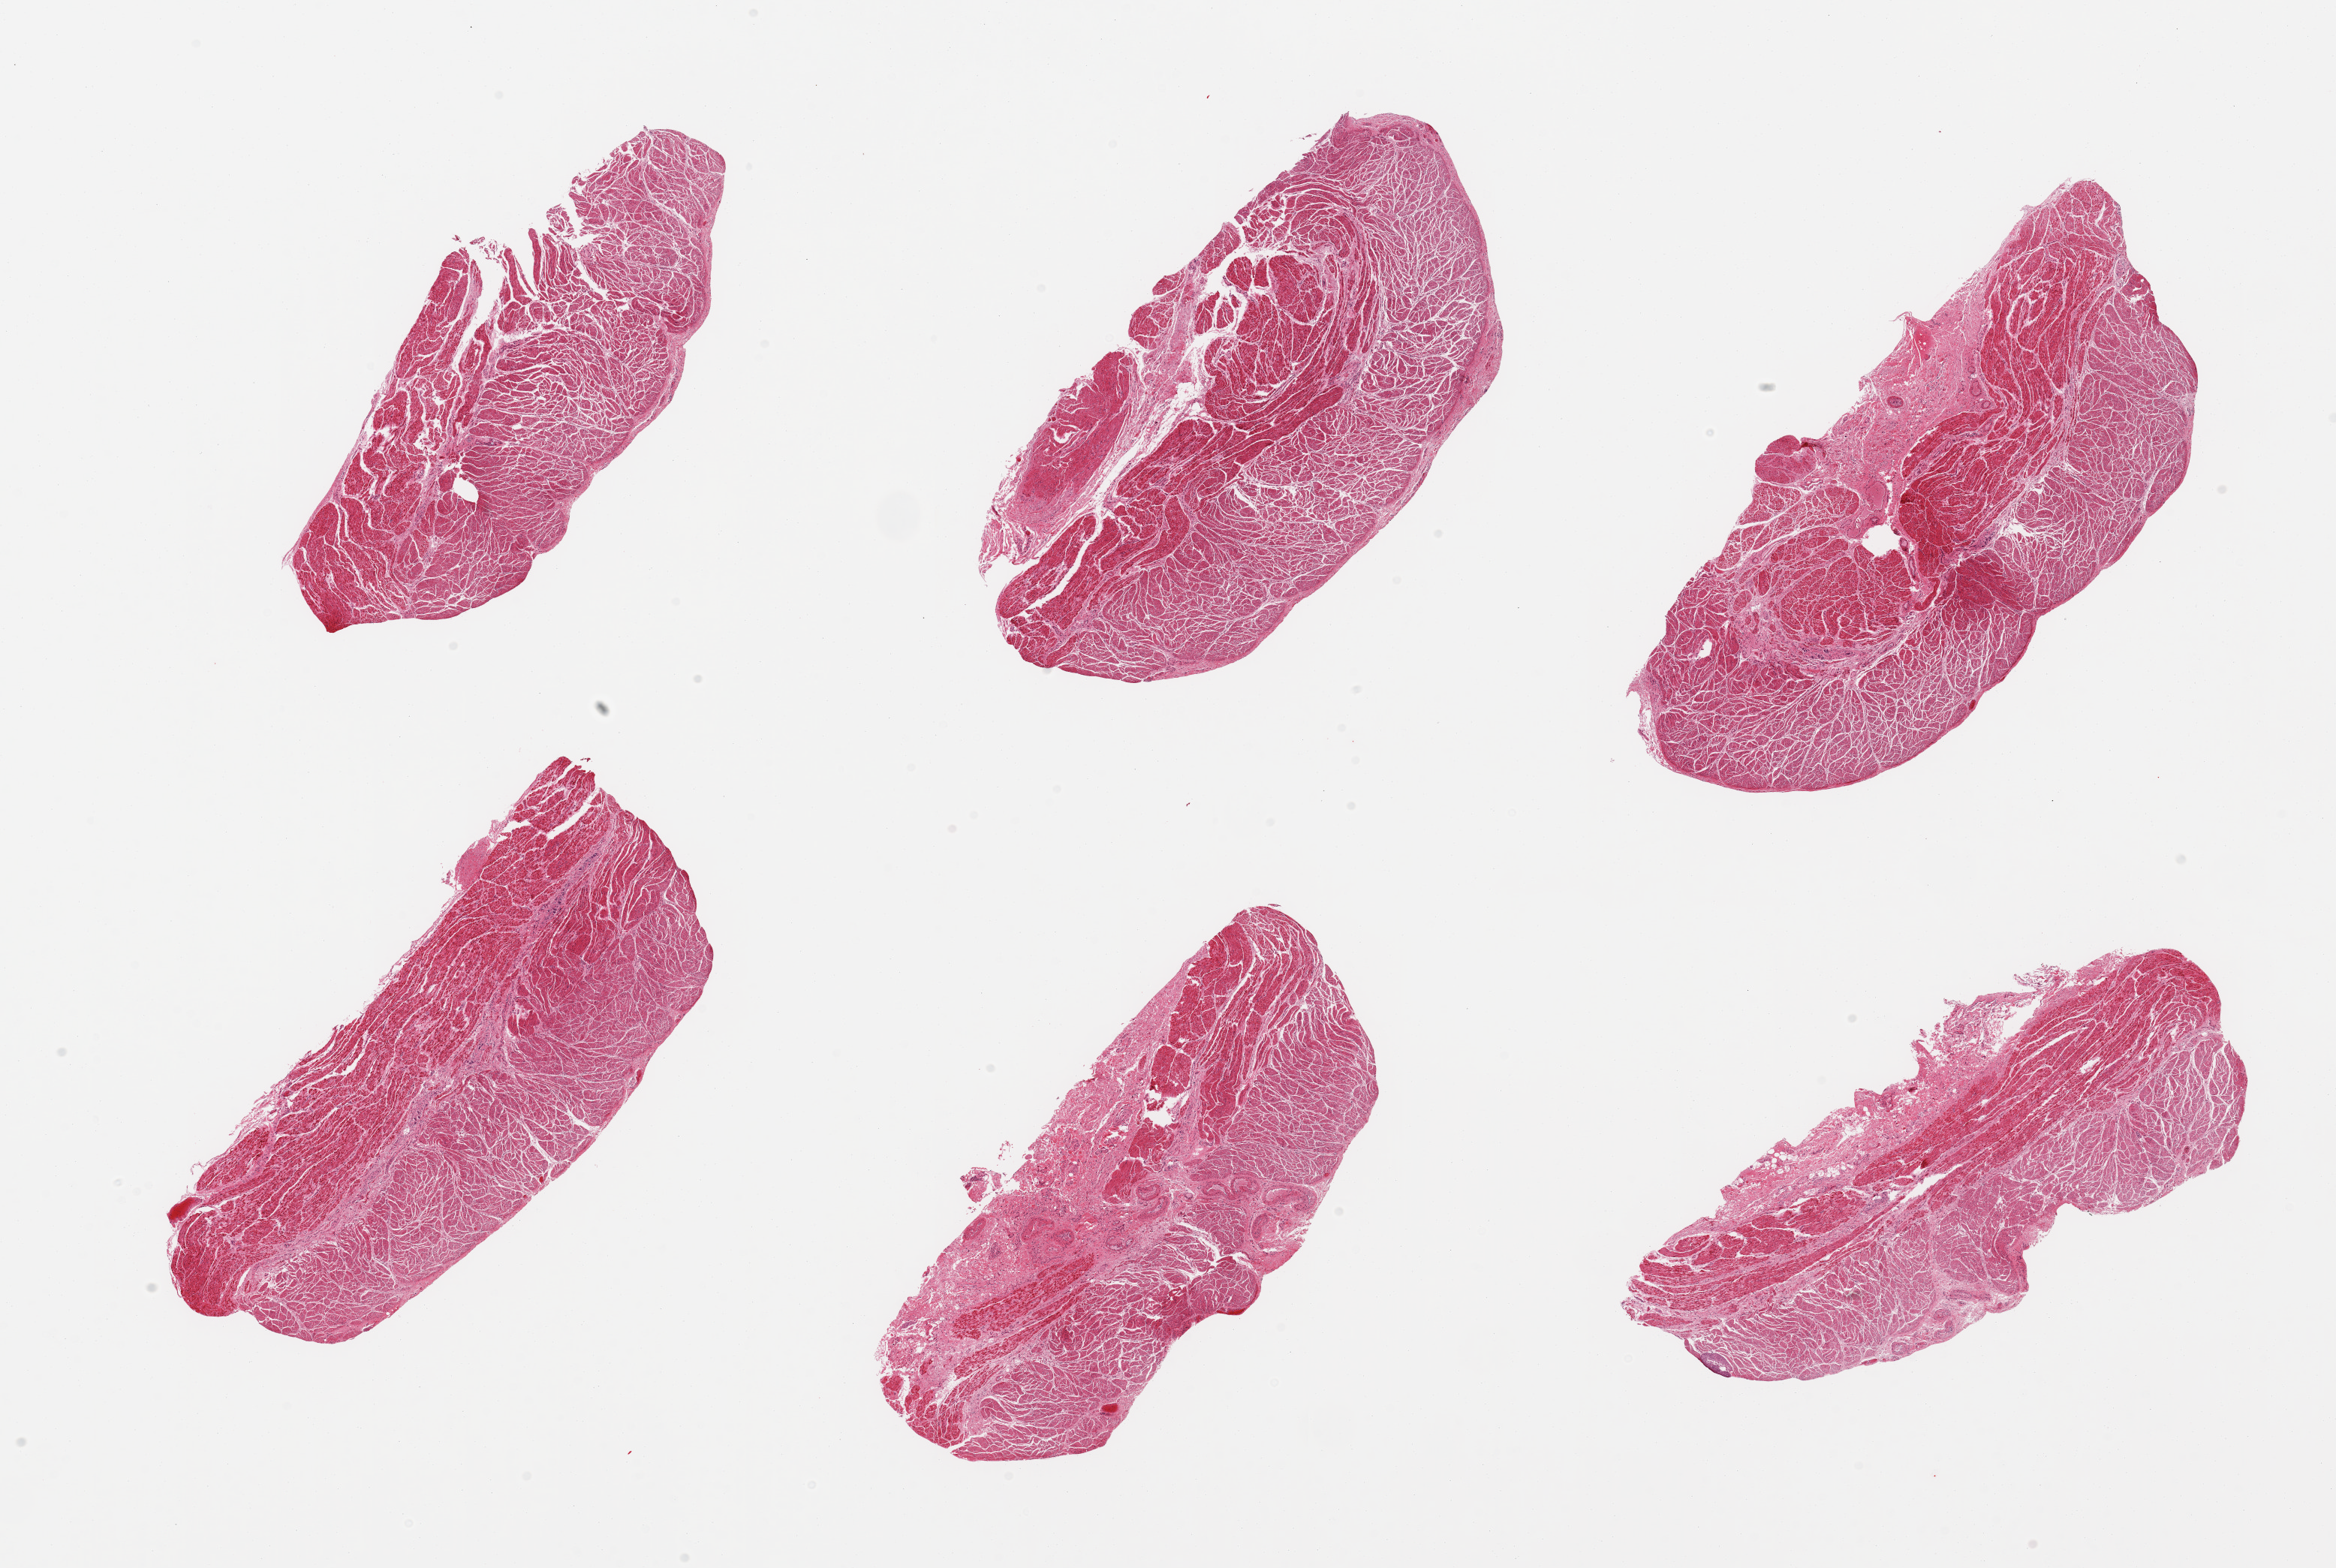
Digitized hematoxylin and eosin (H&E)-stained section, brightfield, a low-resolution overview of the entire scanned area, about 24.6 x 16.5 mm. PAXgene-fixed paraffin-embedded (PFPE) section. Sampled site (target tissue): gastroesophageal junction. Donor tissue sample. Donor: male.
• review note (as recorded): 6 pieces, confirmed target muscularis